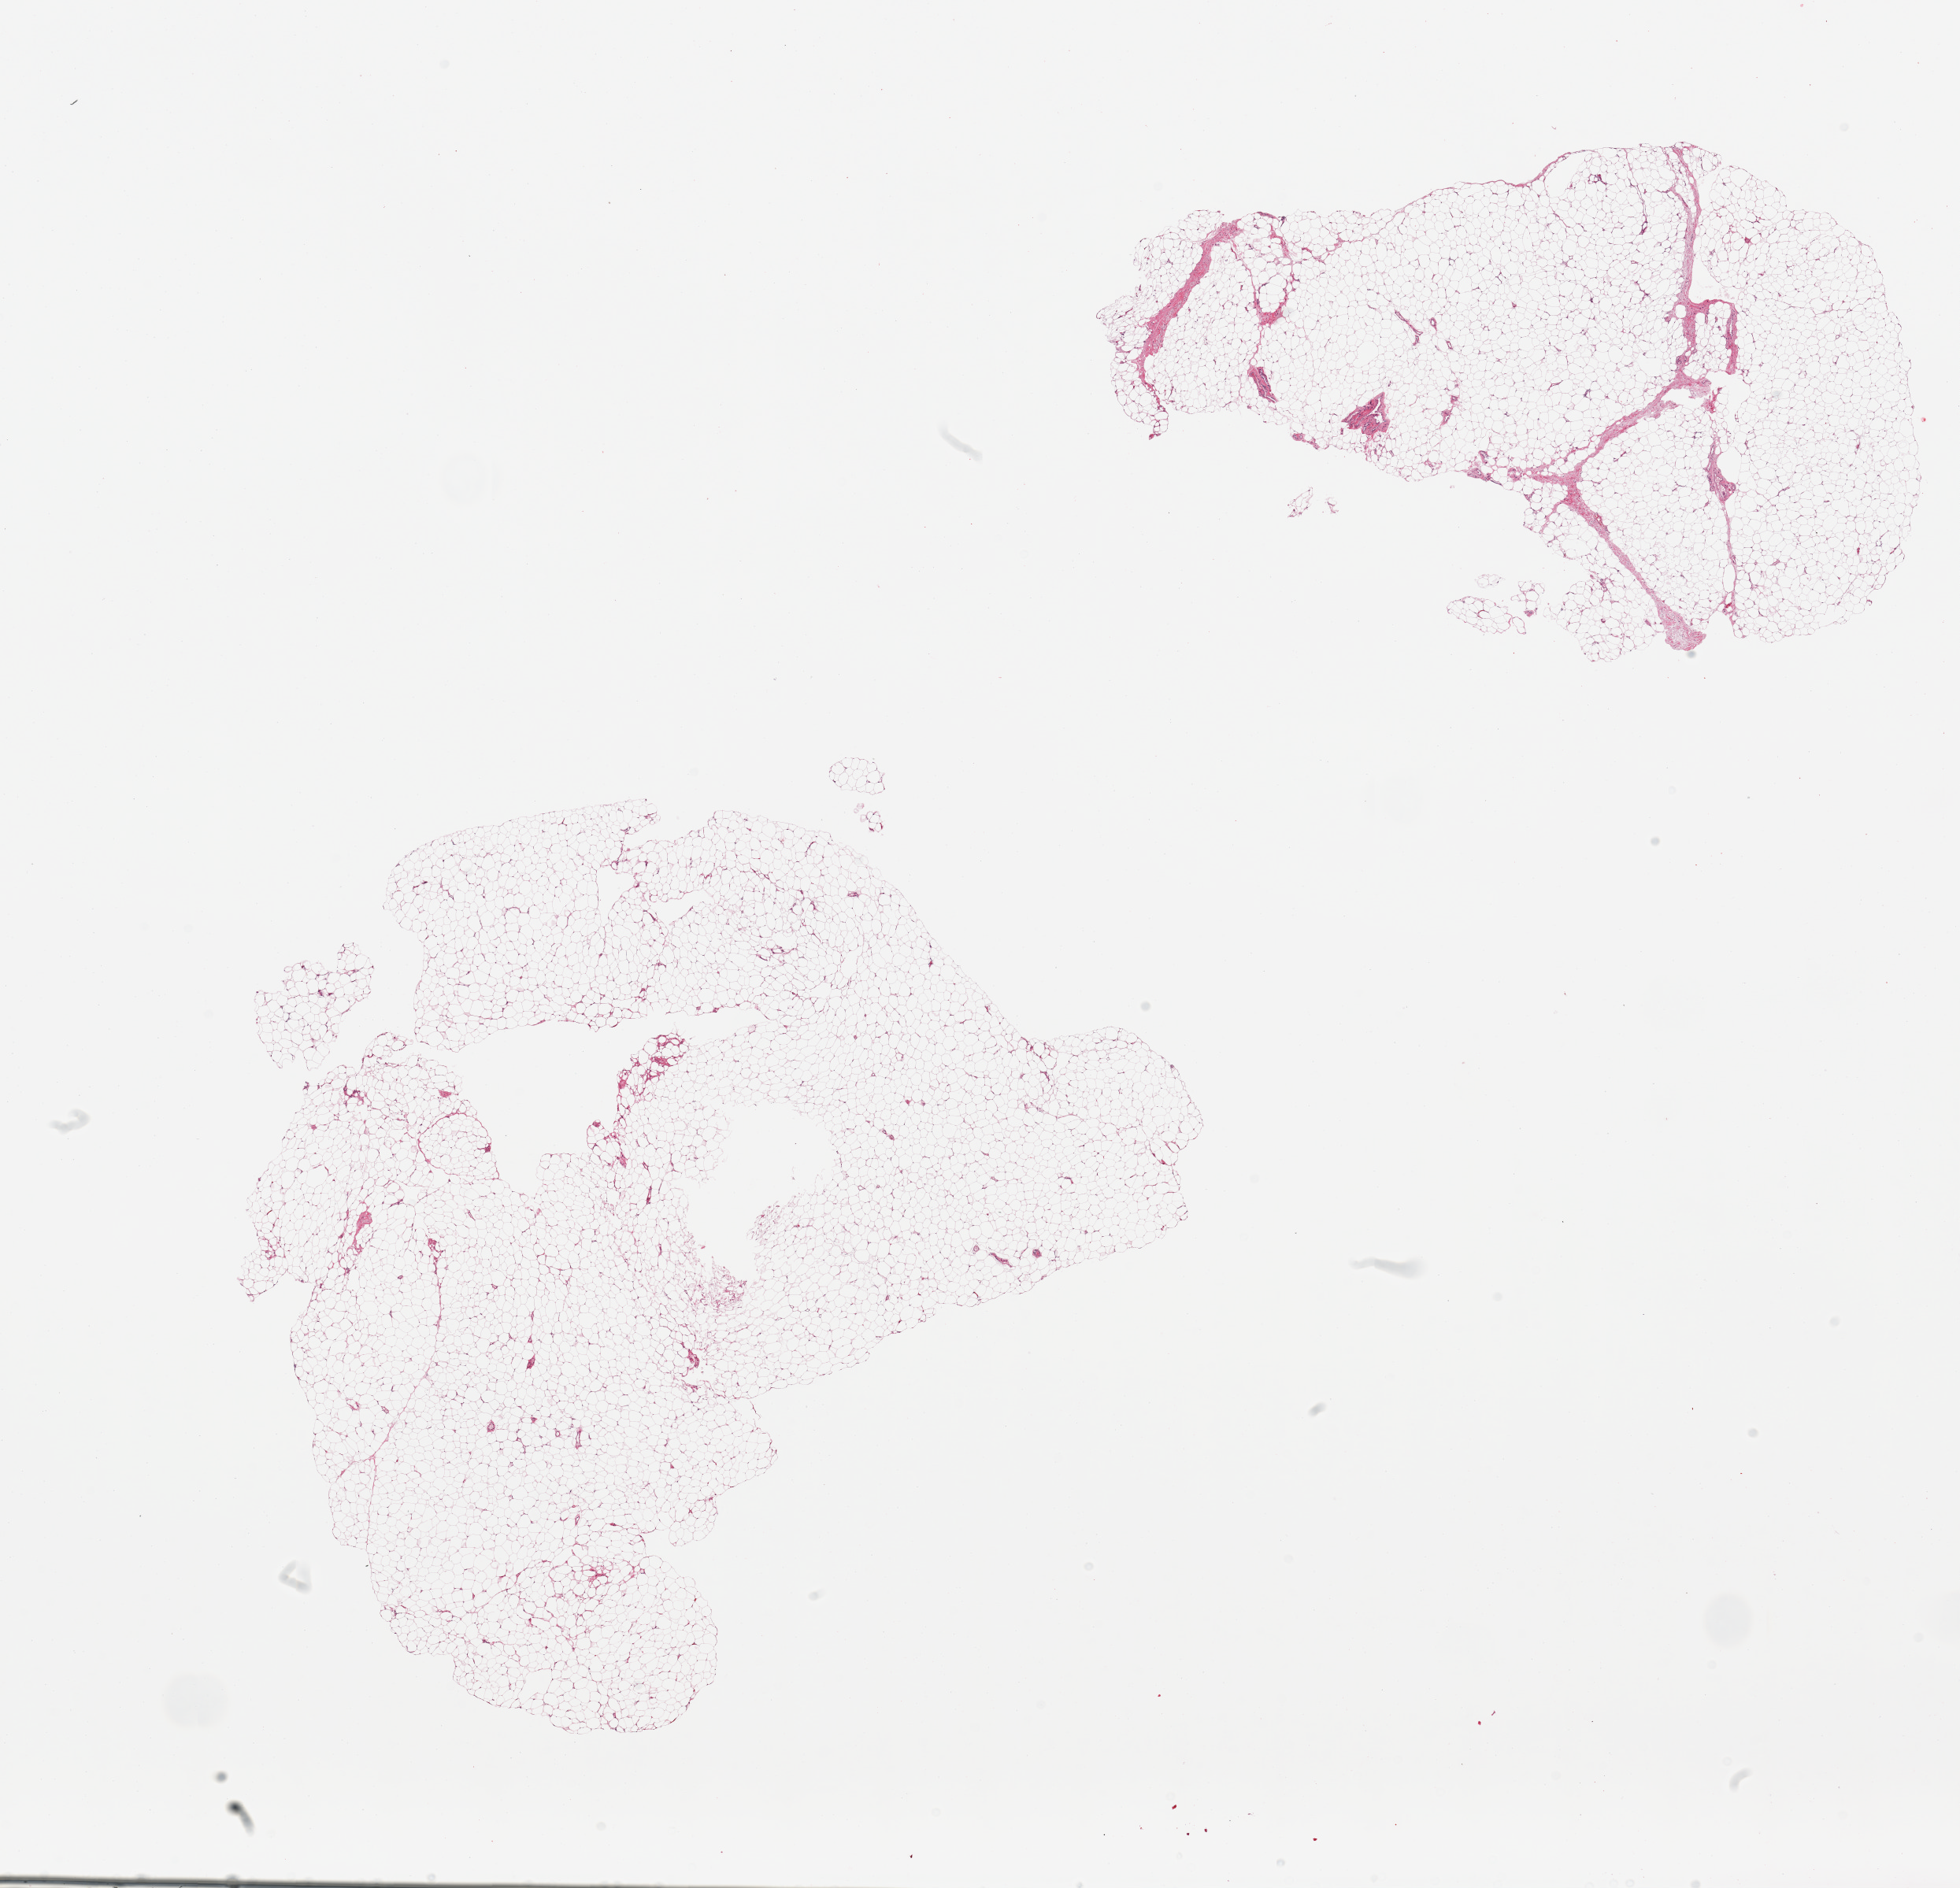
Digitized H&E-stained section — a low-resolution overview of the entire scanned area, about 19.7 x 19.0 mm. PAXgene-fixed paraffin-embedded (PFPE) section. Section of adipose tissue (target tissue). Donor tissue sample. Donor: female.
• review note (as recorded): 2 pieces